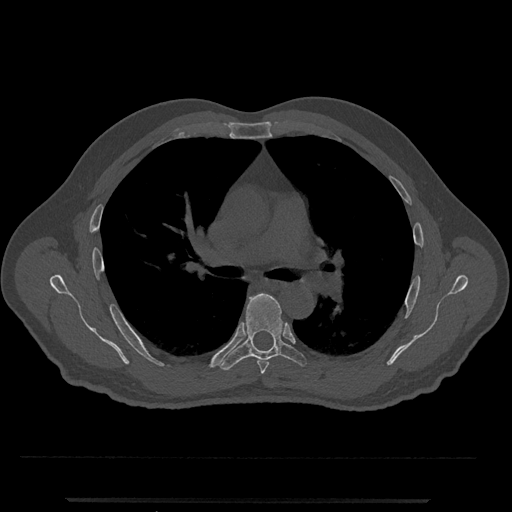
CT including the spine, one axial slice; reconstruction kernel Br40s/3; 120 kVp; bone window (W 1800 / L 400 HU); 512 × 512 image matrix, field of view 419 × 419 mm. Male patient, age 63 years. From the clinical record (not read from this slice): primary cancer: prostate.
Annotated regions visible in this slice (semi-automatic segmentation, software-assisted and operator-edited):
- T5 vertebra: bounding box [x1, y1, x2, y2] px = [257, 360, 269, 374]
- T6 vertebra: [219, 293, 307, 371]